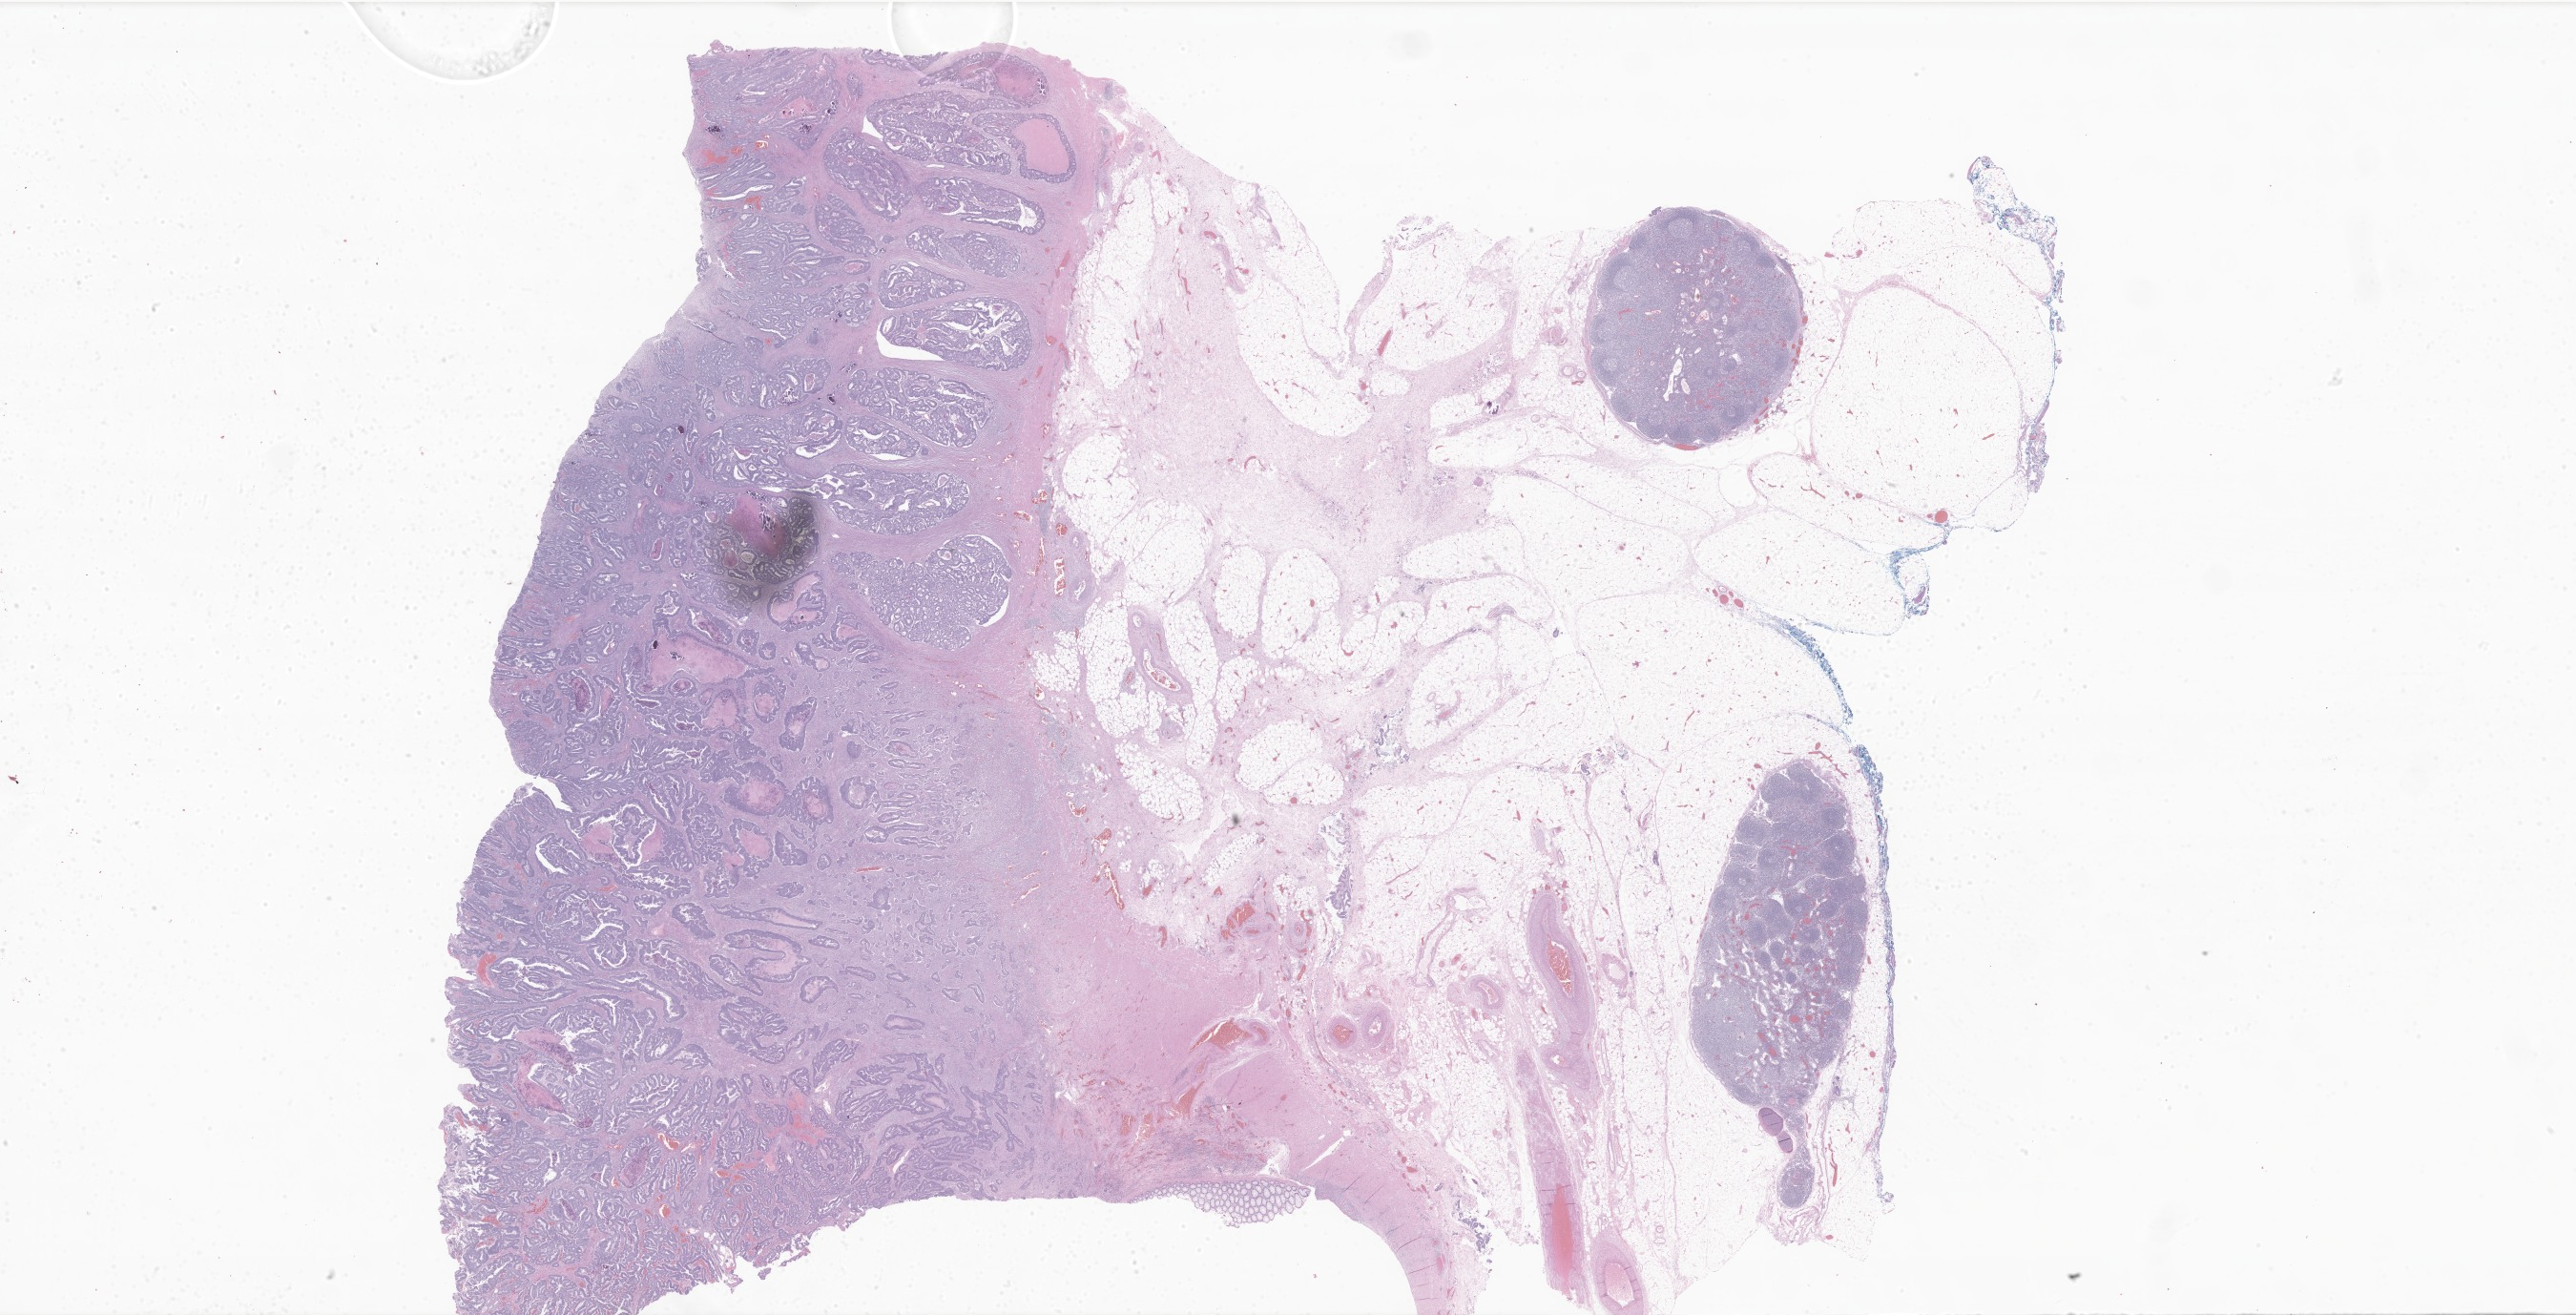
Whole-slide image, hematoxylin and eosin (H&E) stain of tumor tissue from the sigmoid colon, shown as a low-resolution overview of the whole scanned area (about 45.5 x 23.2 mm), formalin-fixed paraffin-embedded section. Patient: male, age 185 months (15 years 5 months).
* recorded diagnosis: Adenocarcinoma in adenomatous polyposis coli